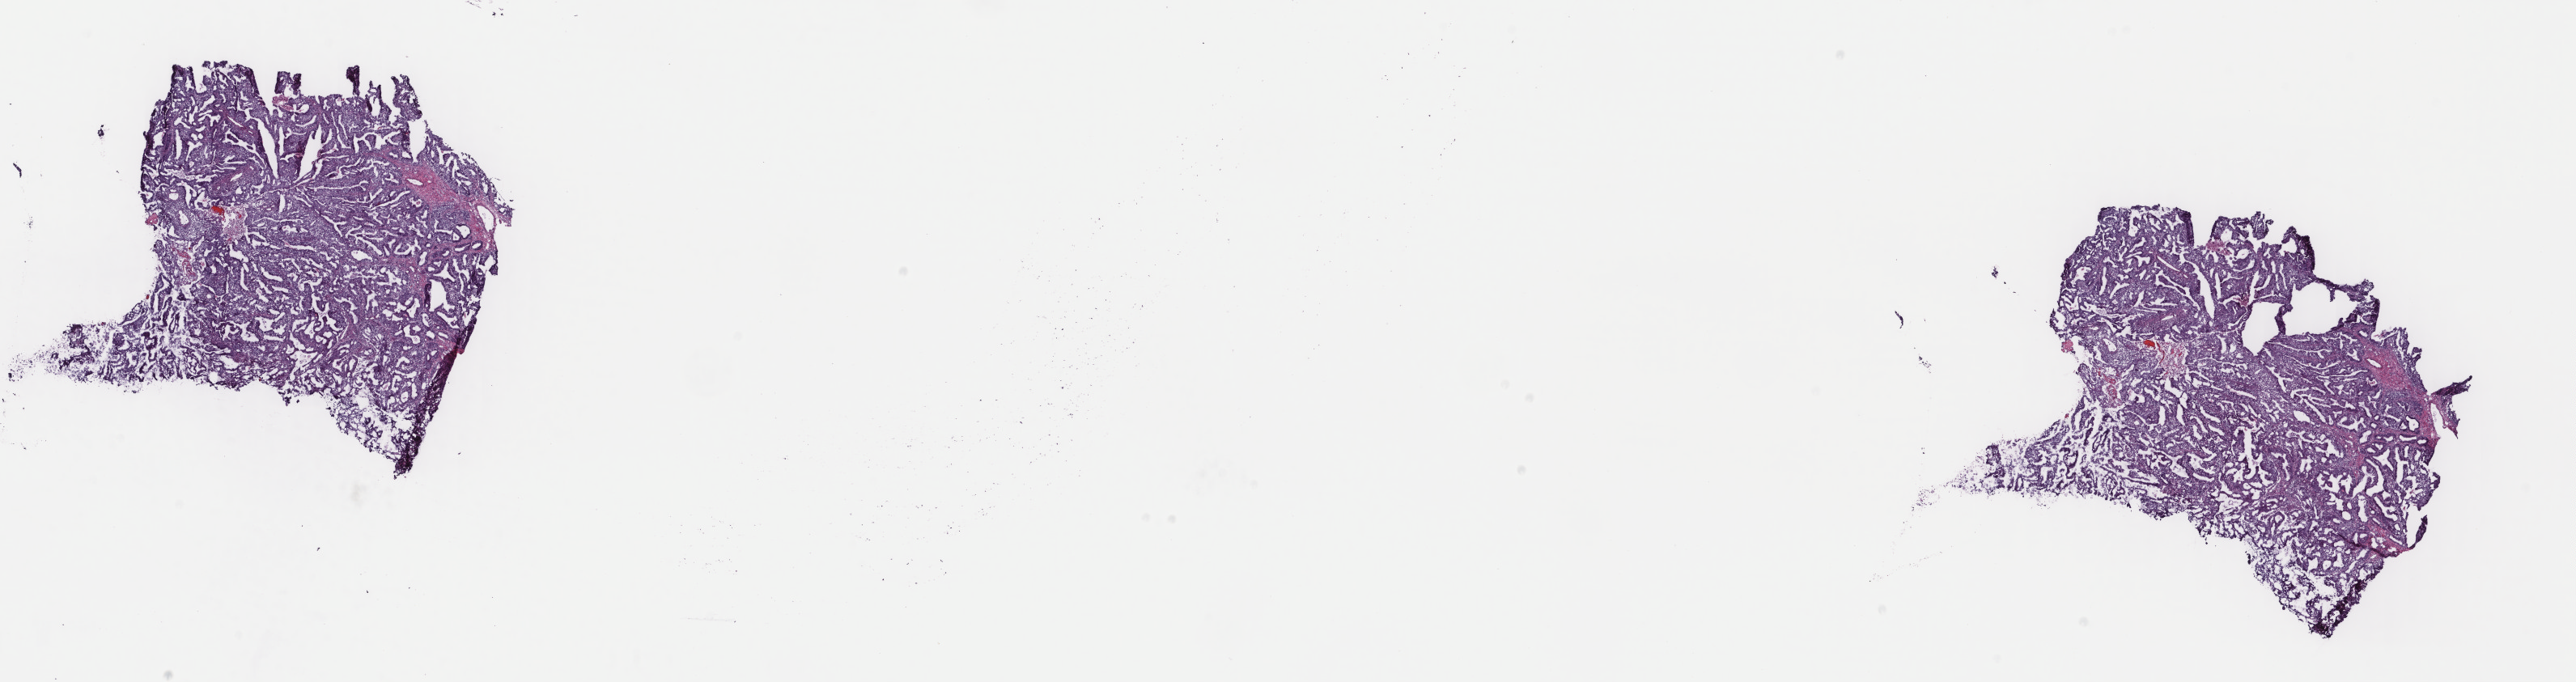
H&E-stained whole-slide image — a low-resolution overview of the entire scanned area, about 25.3 x 6.7 mm, frozen section from the top of the tissue portion, sample: primary tumour, uterus. Female patient; age at initial diagnosis 39 years. Histologic grade: G1 (well differentiated). Composition of this section per pathologist review: tumour cells 50%, tumour nuclei 70%, normal cells 10%, stromal cells 20%, necrosis 20%. Infiltration values recorded for this section: lymphocyte infiltration 10%, monocyte infiltration 0%, neutrophil infiltration 0%.
* FIGO stage: IA
* histologic diagnosis: Endometrioid adenocarcinoma, NOS (endometrium)